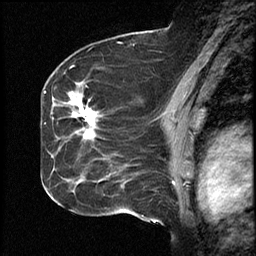
Breast MRI (dynamic contrast-enhanced), one sagittal slice; position 28 of 46 along the scan axis; dynamic contrast-enhanced study with each time point stored as its own series, time point 2 of 4 at this slice position (early post-contrast, ordered by acquisition time); 1.5 T; TE 4.2 ms, TR 18.3 ms; 3 mm slice thickness; 256 × 256 image matrix, field of view 200 × 200 mm. Case-level facts recorded for this patient, not image findings: setting: breast cancer imaged before/during neoadjuvant chemotherapy; receptor status: HR-positive, HER2-negative.
Structures marked on this image (semi-automatic segmentation, software-assisted and operator-edited):
- analysis volume of interest (the breast-tissue region the enhancement analysis was run in; not a lesion): bounding box (x1, y1, x2, y2) in pixels: (64, 72, 111, 197)
- tumour enhancement mask (voxels above the 100 % enhancement threshold inside the analysis volume of interest): (79, 101, 94, 134)